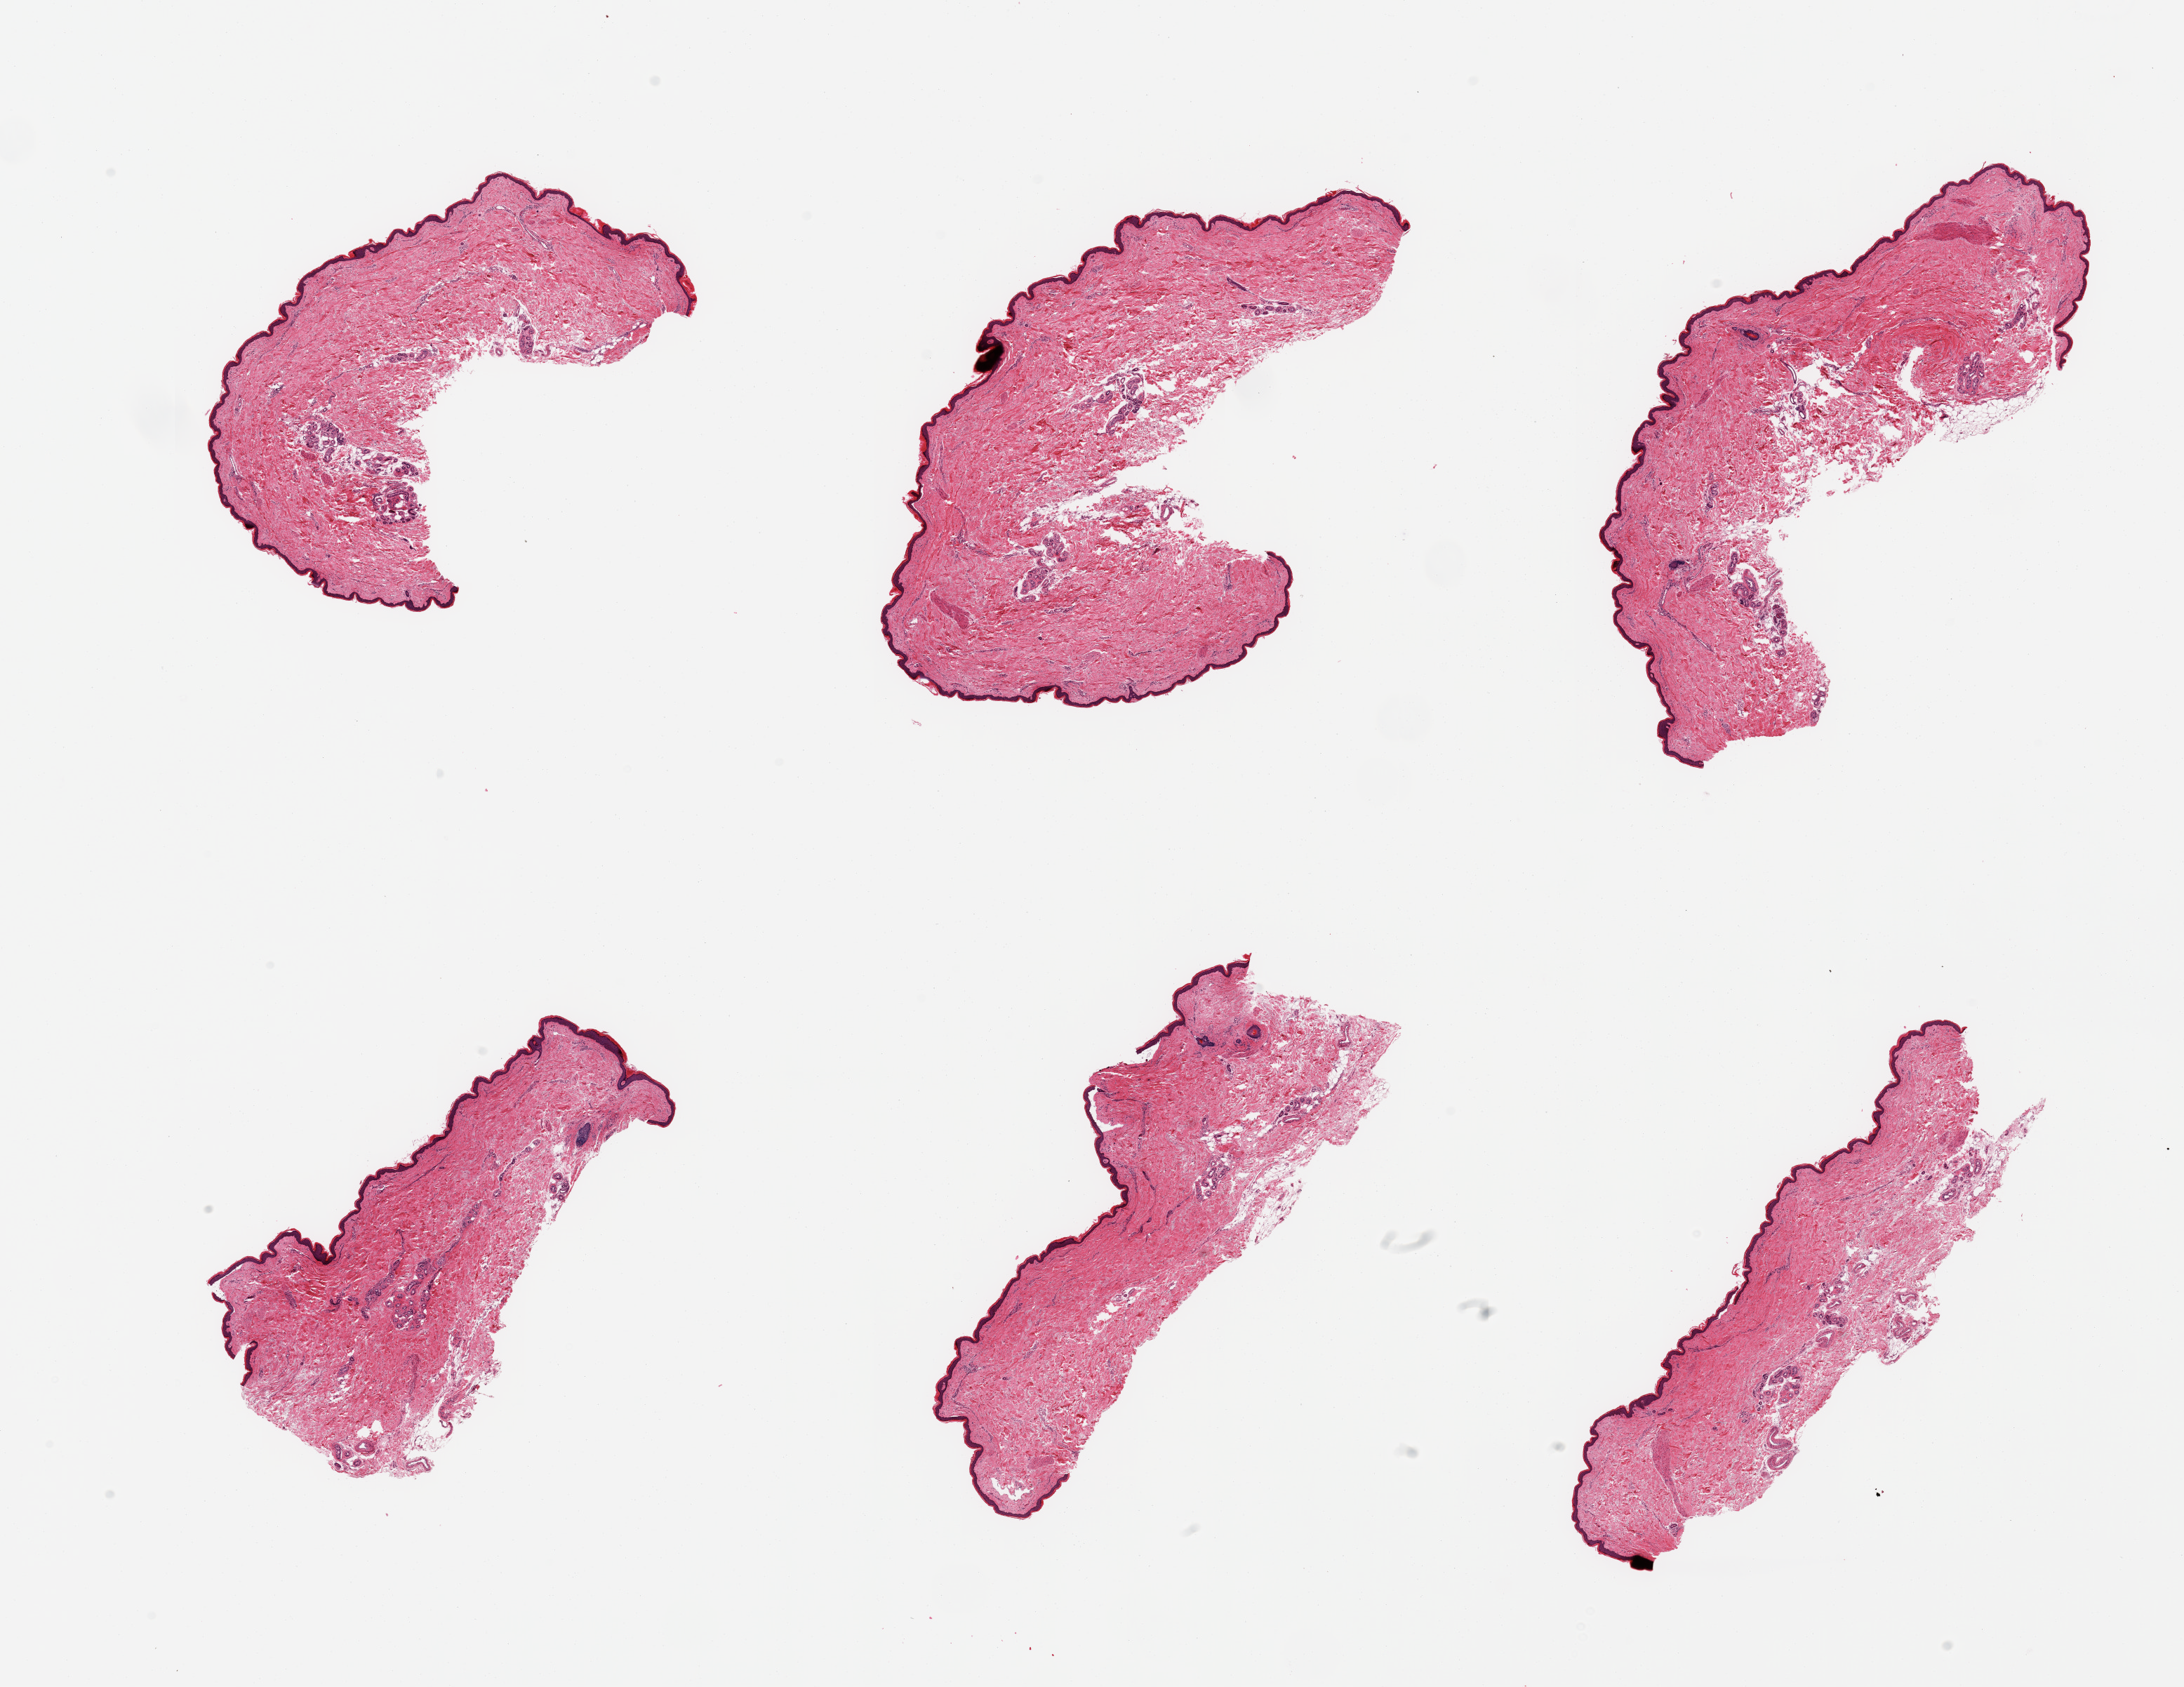
Whole-slide image, haematoxylin and eosin stain, whole scanned area (about 24.6 x 19.0 mm) shown as a low-resolution overview. PAXgene-fixed paraffin-embedded (PFPE) section. Sampled site (target tissue): skin of lower leg. Donor tissue sample. Donor: male.
• review note (as recorded): 6 pieces; well trimmed; minimal dermal fat